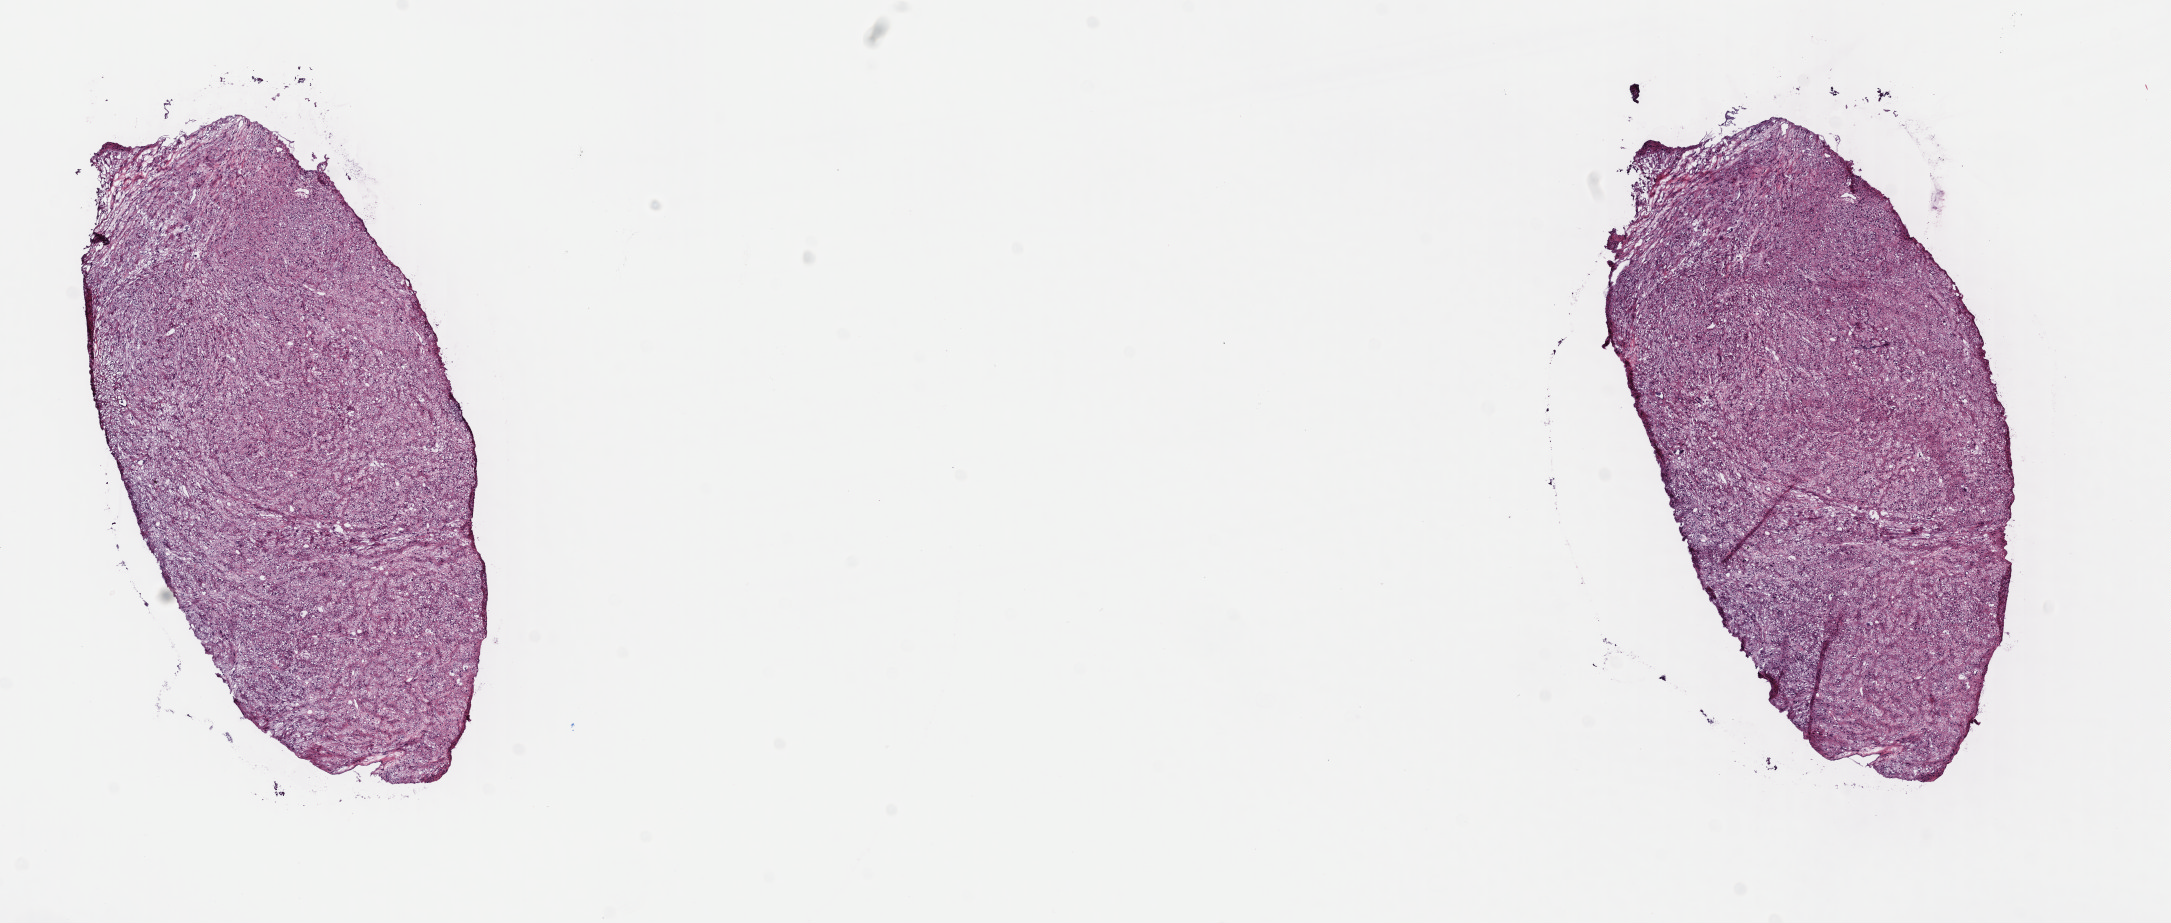
Digitized H&E tissue section (whole slide), whole scanned area (about 17.1 x 7.3 mm, slide scanned at 40x) shown as a low-resolution overview; frozen section from the top of the tissue portion; sample: primary tumour, retroperitoneum and peritoneum. Female patient; age at initial diagnosis 58 years. Composition of this section per pathologist review: tumour cells 80%, tumour nuclei 100%, normal cells 0%, stromal cells 20%, necrosis 0%. Inflammatory infiltration, as recorded: lymphocyte infiltration 0%, monocyte infiltration 0%, neutrophil infiltration 0%.
Pathologic diagnosis: Leiomyosarcoma, NOS.